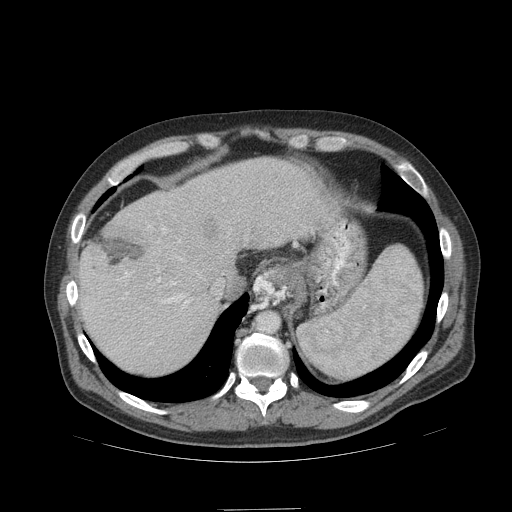
Contrast-enhanced abdominal CT (liver protocol), one axial slice. Position 81 of 99 along the scan axis. Reconstruction kernel STANDARD. 140 kVp. Soft-tissue window (W 400 / L 40 HU). 2.5 mm slice thickness. 512 × 512 image matrix, field of view 440 × 440 mm. Case-level facts recorded for this patient, not image findings: diagnosis: hepatocellular carcinoma (patient treated with transarterial chemoembolisation; whether this scan precedes or follows treatment is not stated here); TNM stage (as recorded): Stage-I; Child-Pugh class: A; tumour differentiation: no biopsy.
Outlined on this slice (semi-automatically segmented with operator editing):
- liver parenchyma outside the tumour (the mass and vessels are separate outlines, so this box may not span the whole liver): bounding box (x1, y1, x2, y2) in pixels: (78, 157, 338, 374)
- mass: (202, 215, 216, 238)
- liver vessels: (122, 199, 225, 345)